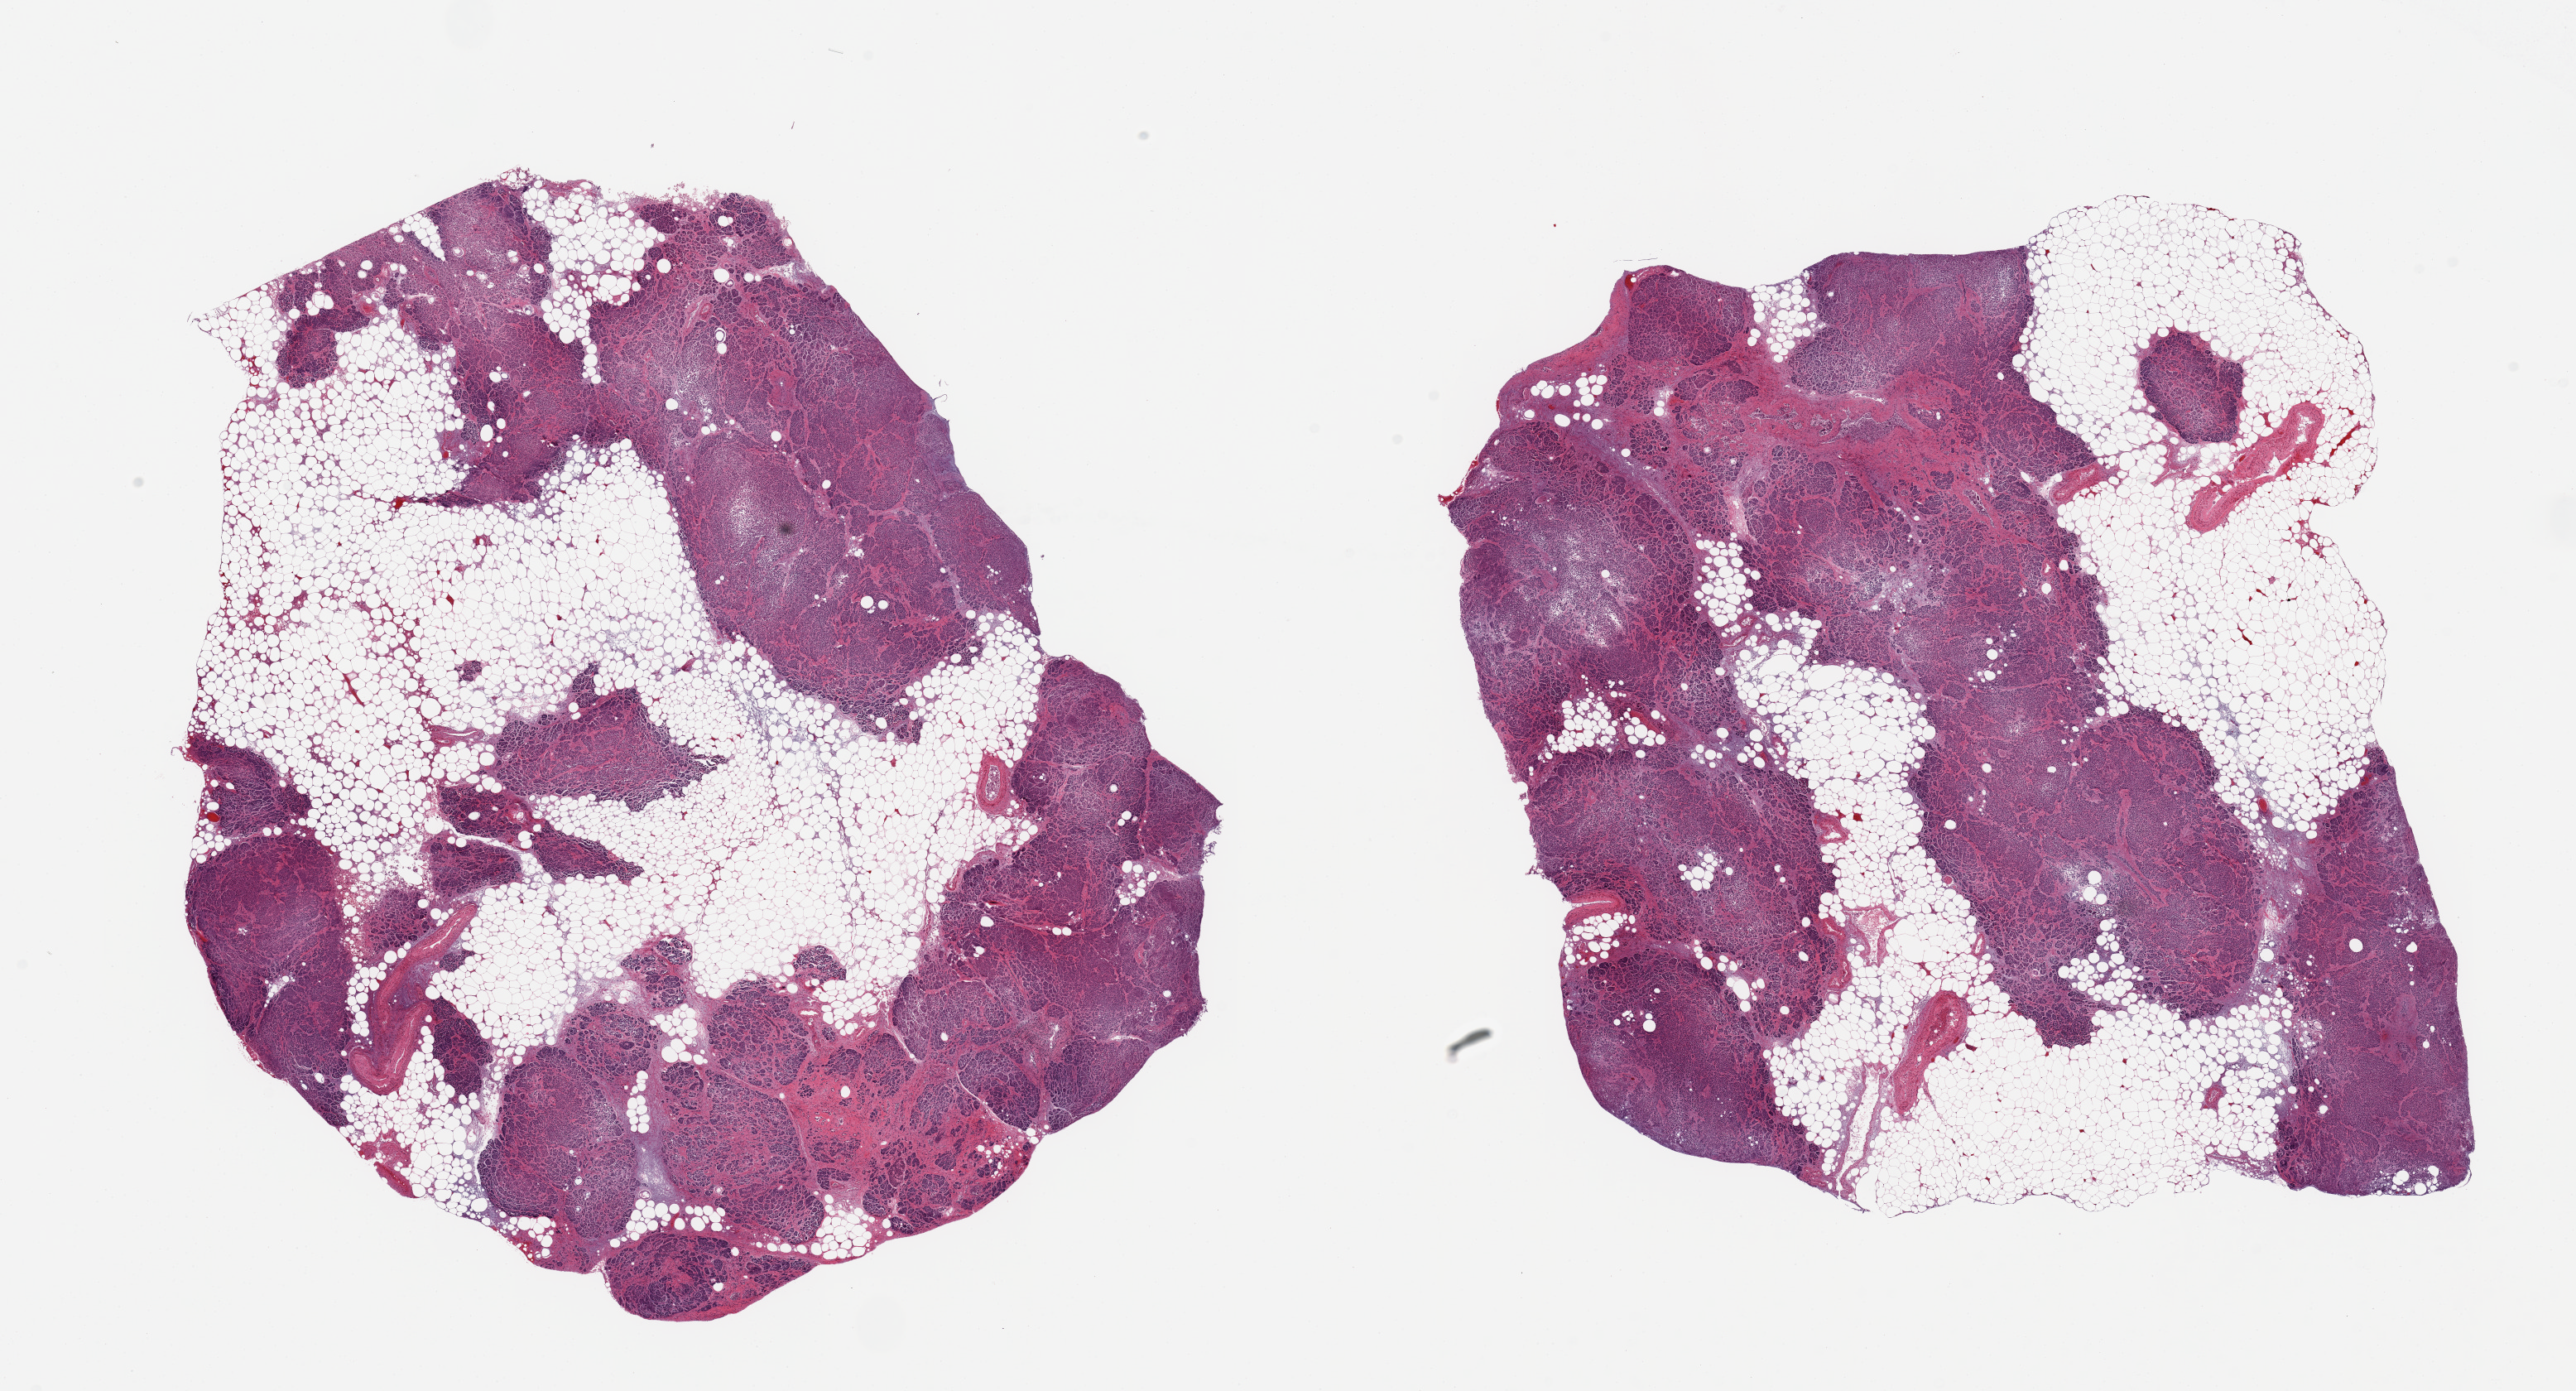
Digitized haematoxylin and eosin-stained section, brightfield, low-resolution overview of the scanned area, about 24.6 x 13.3 mm; PAXgene-fixed paraffin-embedded (PFPE) section; sampled site (target tissue): pancreas; tissue donor sample. Donor sex: male.
Review note (as recorded): 2 pieces, severe autolysis/saponfication. Evidence of remote pancreatitis; ~50% fat. Islets not visible.